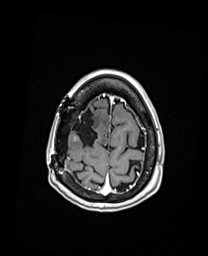
Brain MRI from a brain-tumour surgery series, one axial slice. Position 35 of 192 along the scan axis. T1-weighted post-contrast. 1 mm slice thickness. 208 × 256 image matrix. From the clinical record (not read from this slice): histopathology: Oligodendroglioma; WHO grade: 3; IDH mutation: yes.
Structures marked on this image (manually delineated by an expert):
- previous resection cavity: bounding box (x1, y1, x2, y2) in pixels: (72, 109, 99, 148)